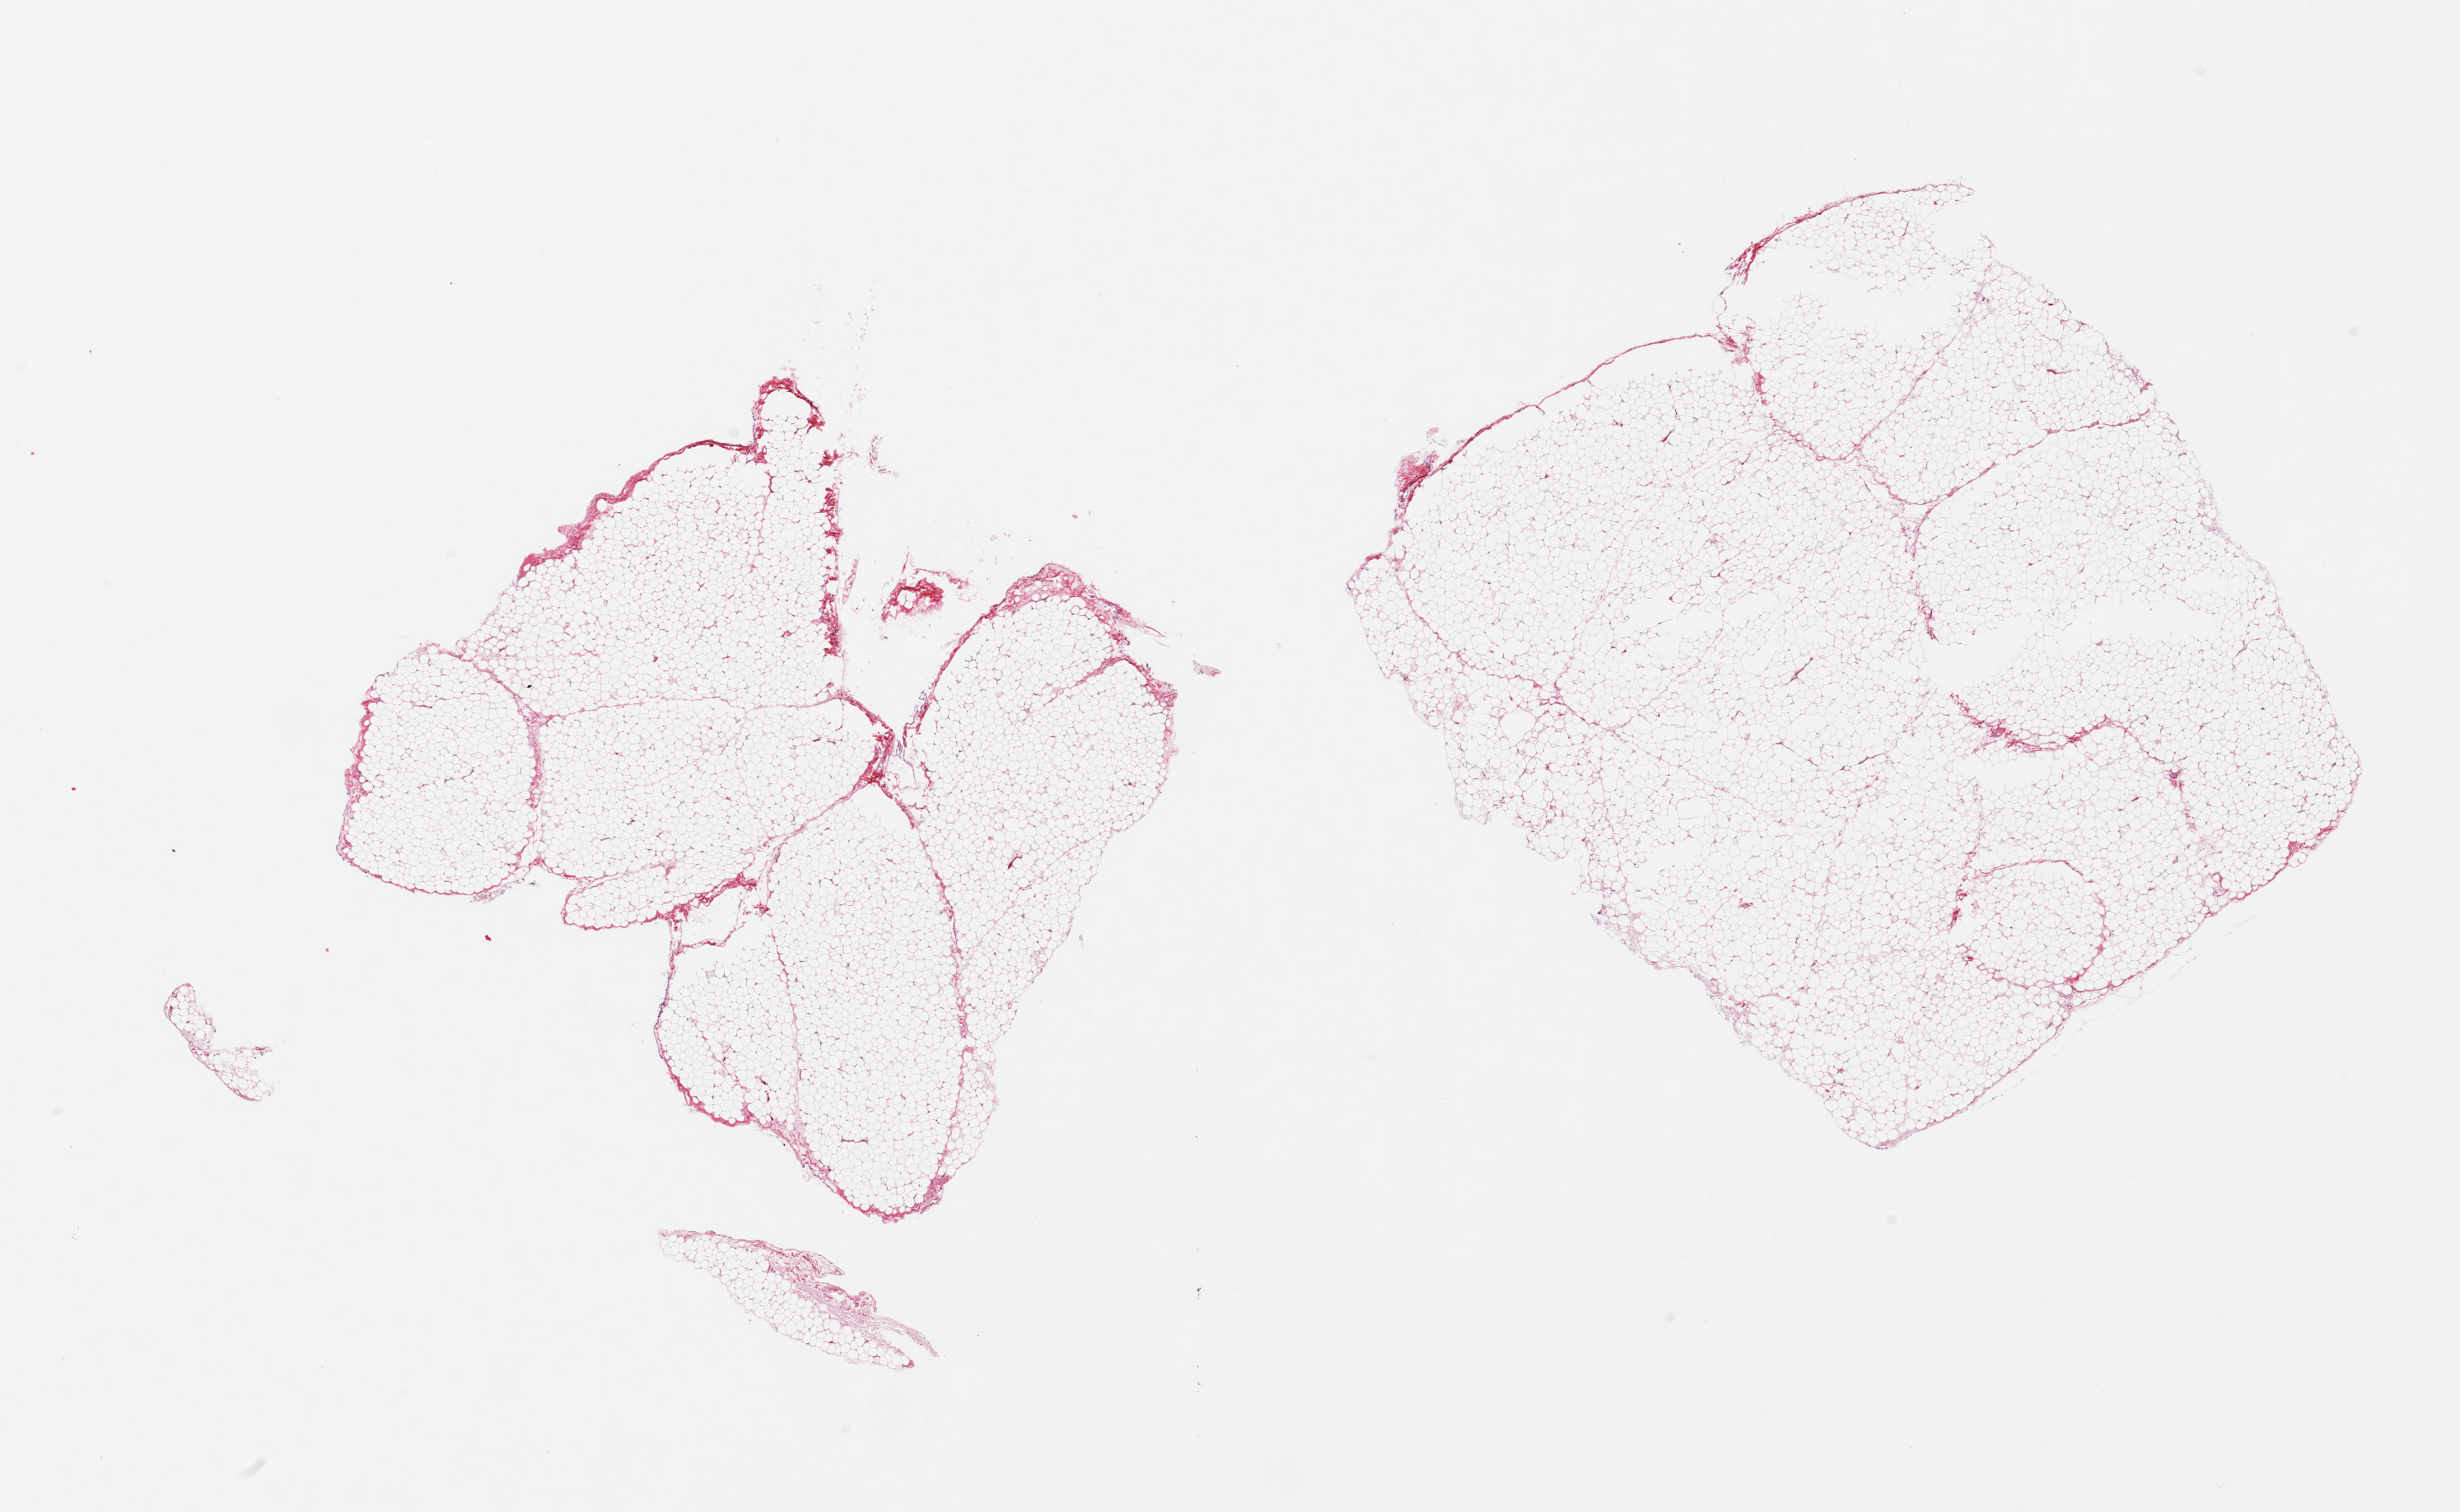
Digitized haematoxylin and eosin-stained section — whole scanned area (about 23.6 x 14.5 mm, slide scanned at 20x) shown as a low-resolution overview; PAXgene-fixed, paraffin-embedded tissue; section of omentum (target tissue); tissue donor sample. Donor sex: female.
Pathologist's review note for this sample: 2 pieces; <5% fibrous content.